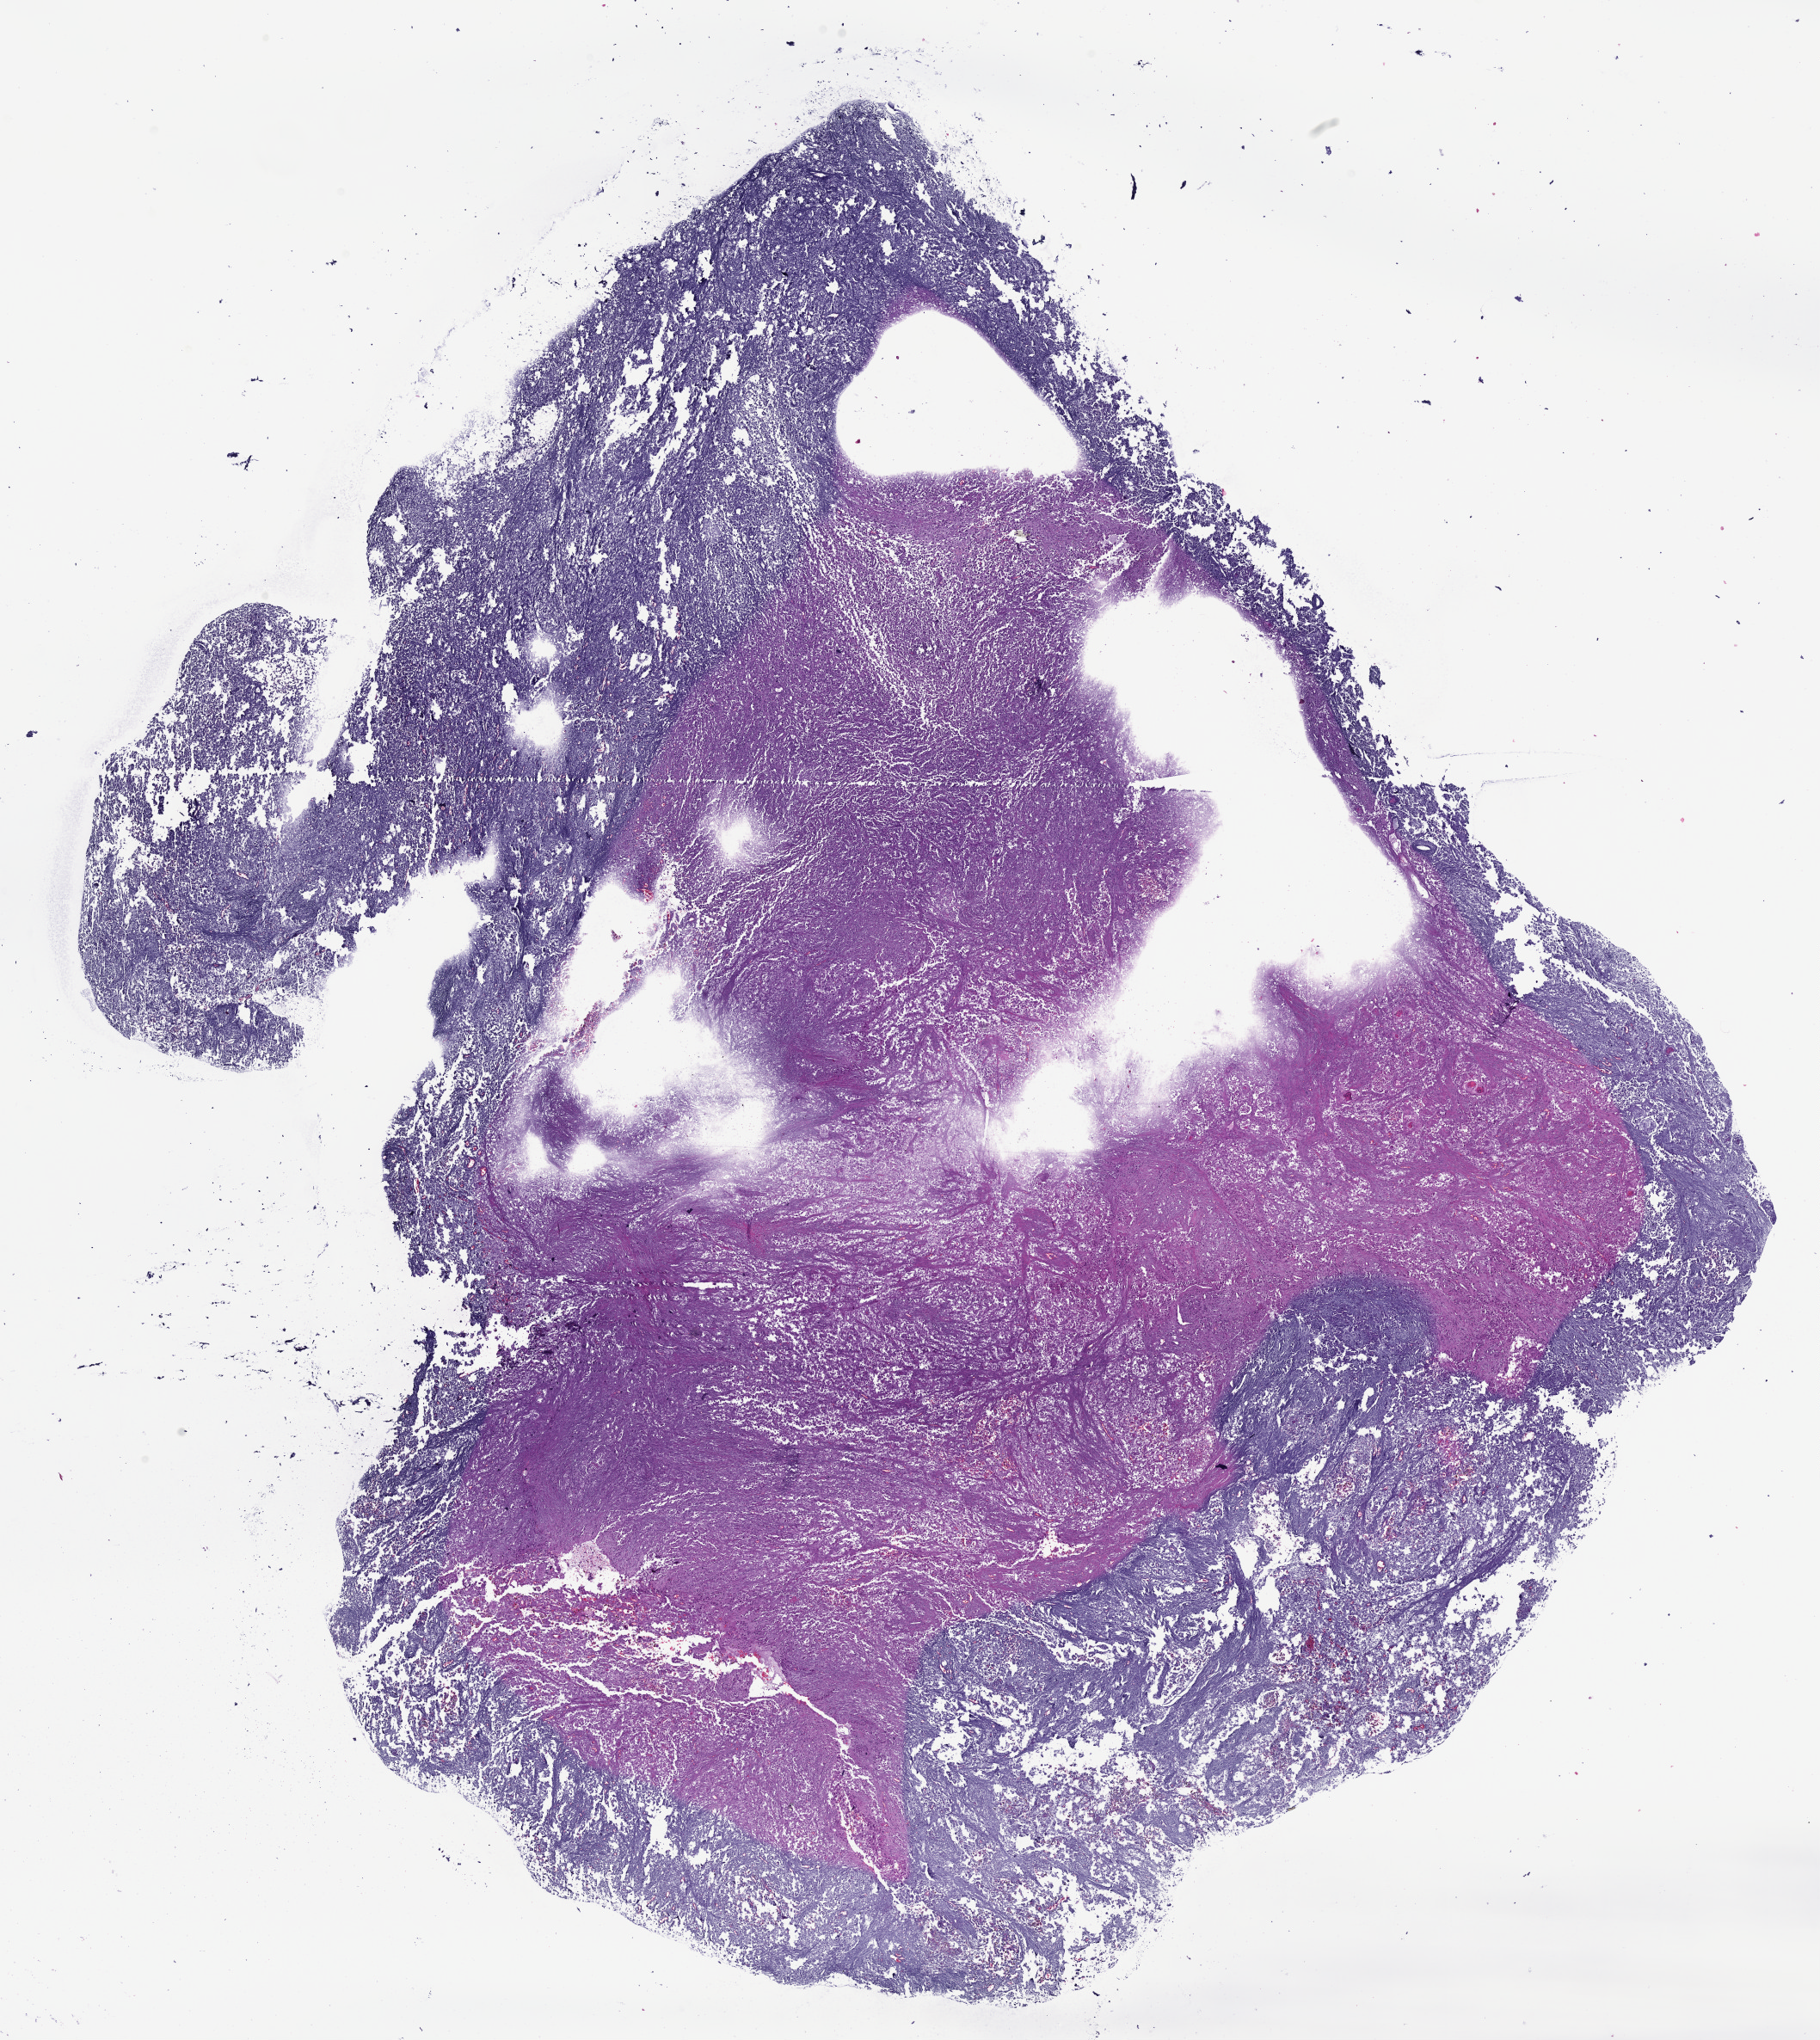
Hematoxylin and eosin (H&E) stained whole-slide image, whole scanned area (about 17.1 x 19.2 mm) shown as a low-resolution overview; formalin-fixed paraffin-embedded (FFPE) diagnostic section; primary tumour sample from the head and neck. Patient: male, age at initial diagnosis 55 years. Histologic grade: G3 (poorly differentiated).
Lymph nodes positive (case pathology): 14 of 24 examined. Laterality: right. Pathologic diagnosis: Squamous cell carcinoma, NOS (overlapping lesion of lip, oral cavity and pharynx). AJCC pathologic stage: IVA.